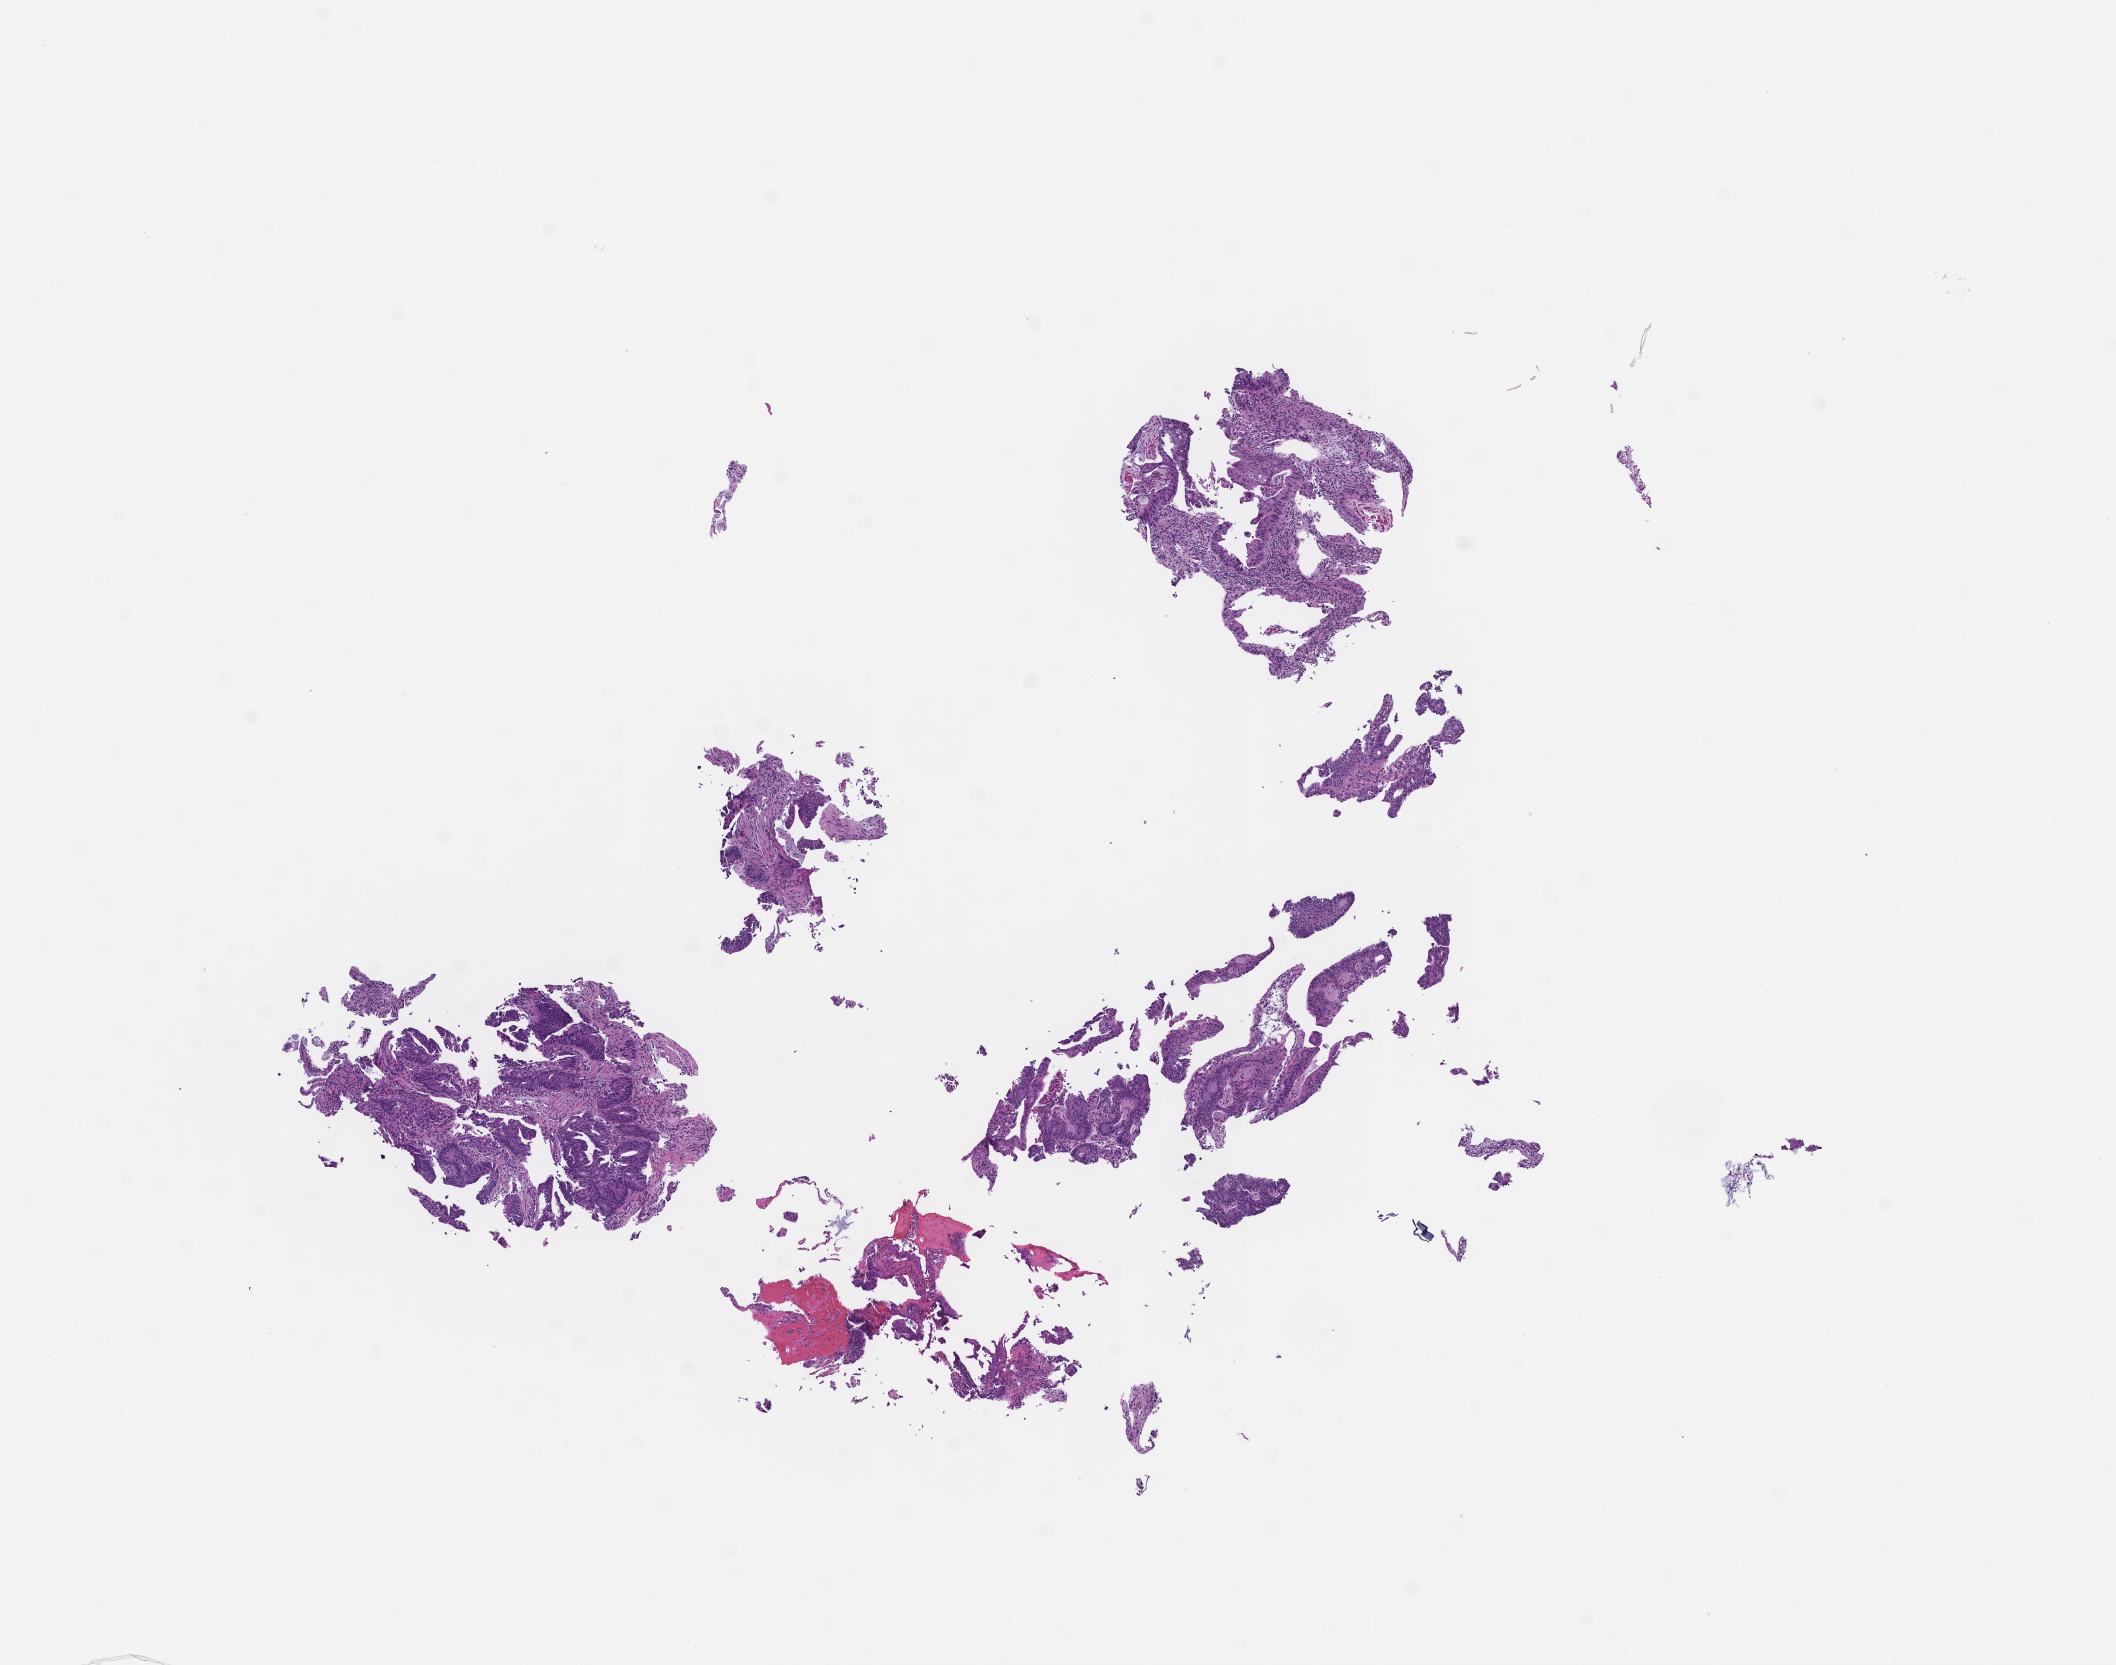
Digitized H&E-stained section — low-resolution overview of the scanned area, about 8.5 x 6.7 mm. Formalin-fixed paraffin-embedded section. Site: colon. Archival tissue. Female patient.
This section: primary tumor. Diagnosis: Colorectal Carcinoma.